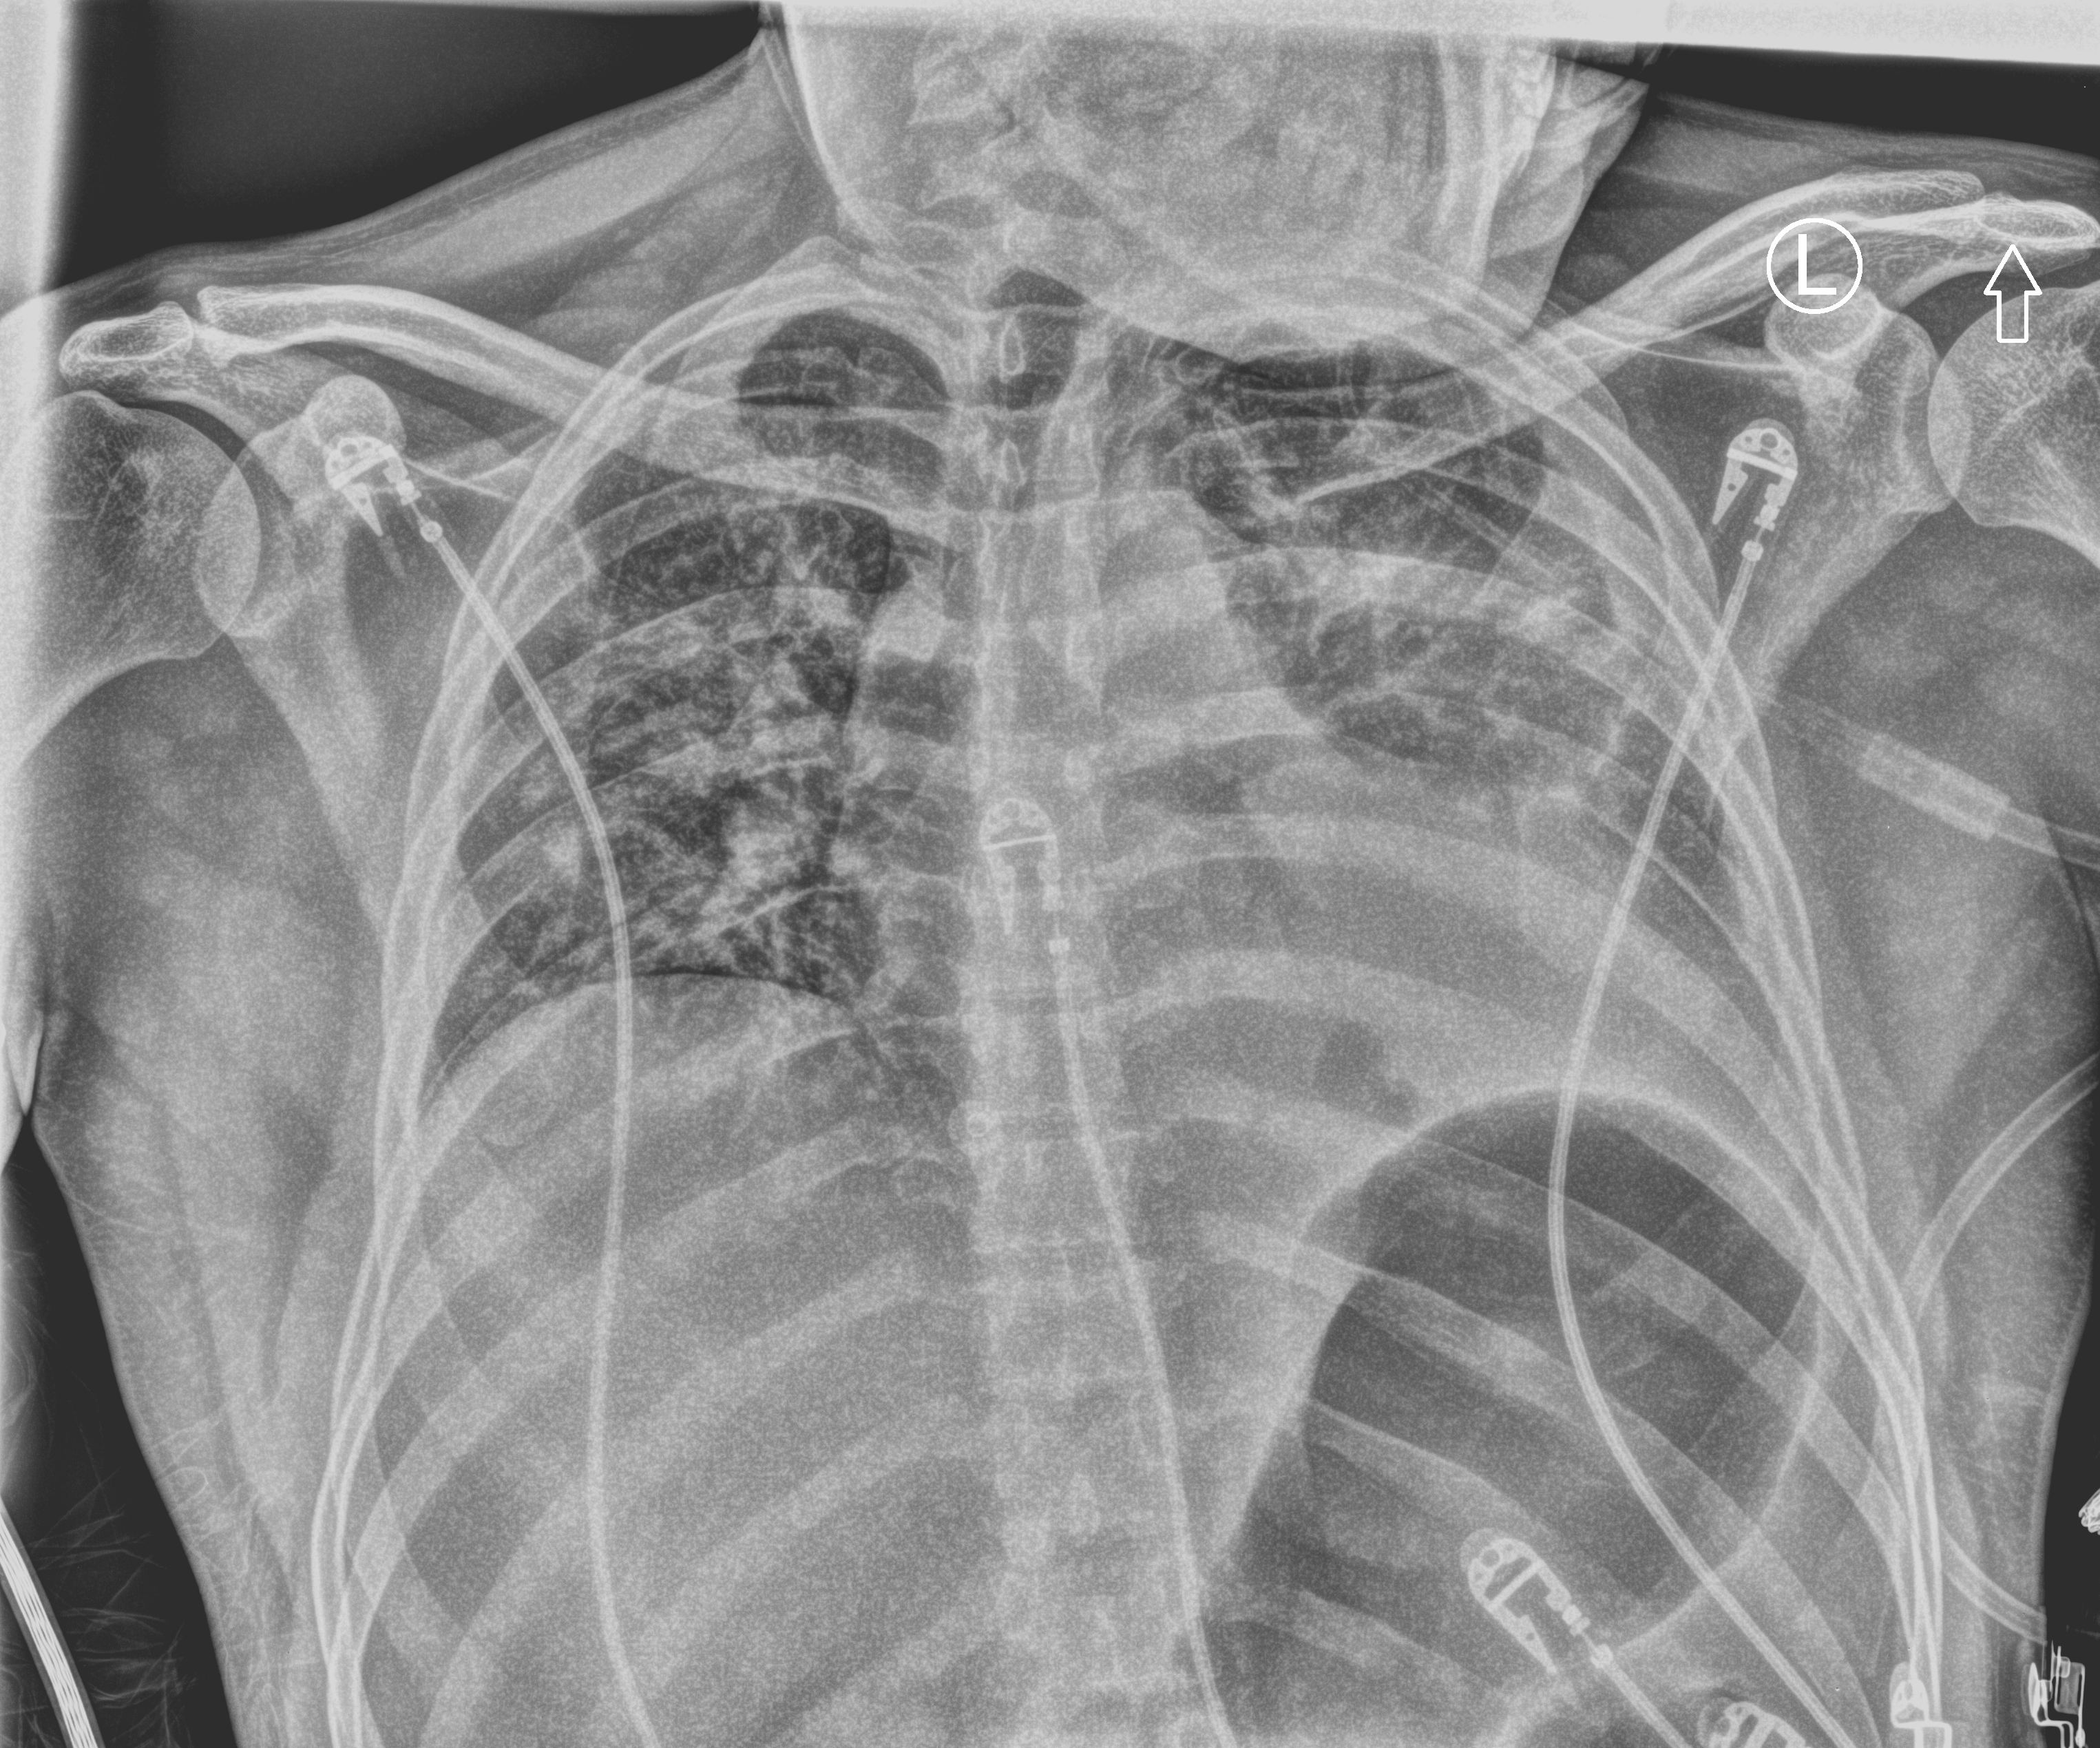
Portable chest radiograph; anteroposterior (AP) projection. Patient hospitalised with COVID-19; male, aged 18–59 years.
From the hospital-stay record, not from the radiograph (when in the stay this image was taken is not recorded): chronic kidney disease (admission record): no; admitted to intensive care during this hospital stay: yes.